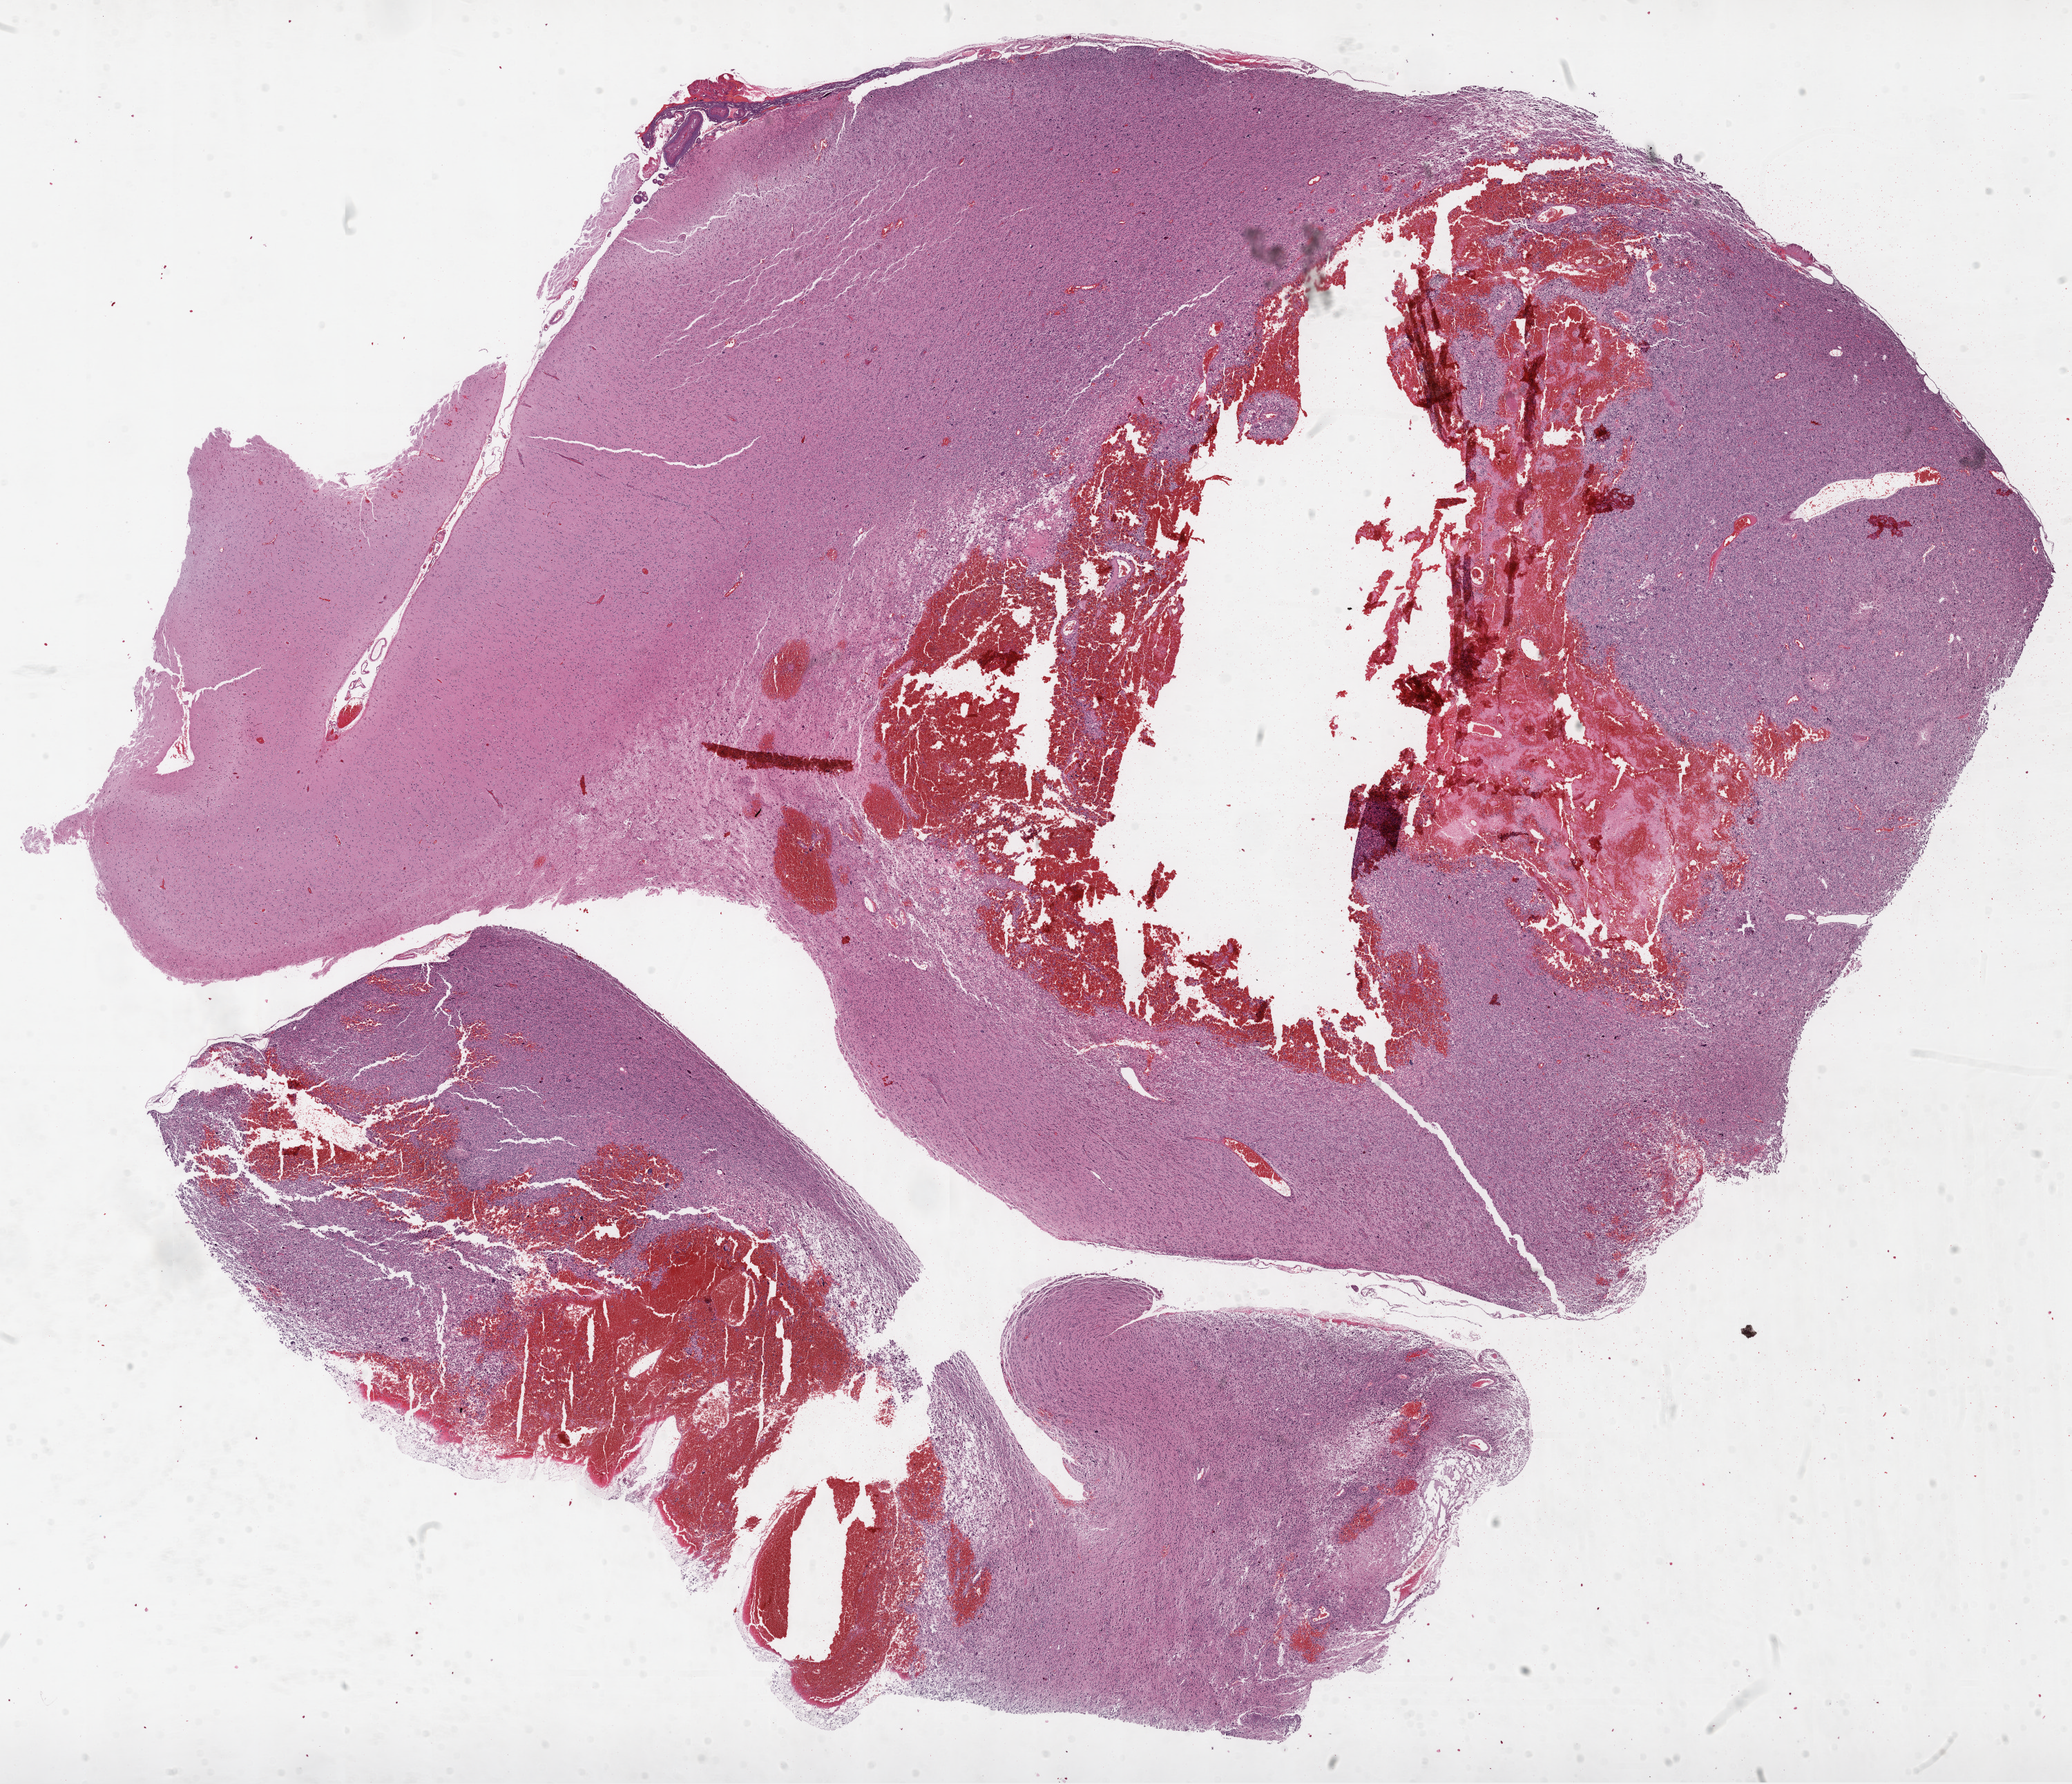
Hematoxylin and eosin (H&E) stained whole-slide image — low-resolution overview of the scanned area, about 24.1 x 20.7 mm. FFPE section. Sample: primary tumour, brain. Male patient; age at initial diagnosis 69 years.
• pathologic diagnosis: Glioblastoma